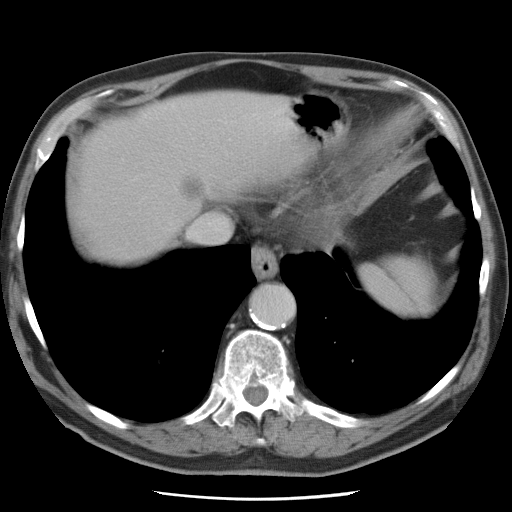
Contrast-enhanced abdominal CT, one axial slice; slice 69 of 78 in the series (ordered by position); 120 kVp; intravenous contrast given; soft-tissue window (W 400 / L 40 HU); 5 mm slice thickness; 512 × 512 image matrix, field of view 337 × 337 mm. Male patient, age 75 years. Case-level facts recorded for this patient, not image findings: diagnosis: colorectal cancer liver metastases, imaged before liver resection; multiple liver metastases: yes; largest metastasis: 2.4 cm; disease in both lobes: yes.
Outlined on this slice (expert manual segmentation):
- hepatic veins: box from (x=189, y=221) to (x=222, y=238) px
- liver: (x=77, y=94)–(x=303, y=262)
- planned liver remnant (the part of the liver to remain after resection): (x=78, y=150)–(x=177, y=265)
- liver metastasis: (x=181, y=177)–(x=206, y=203)